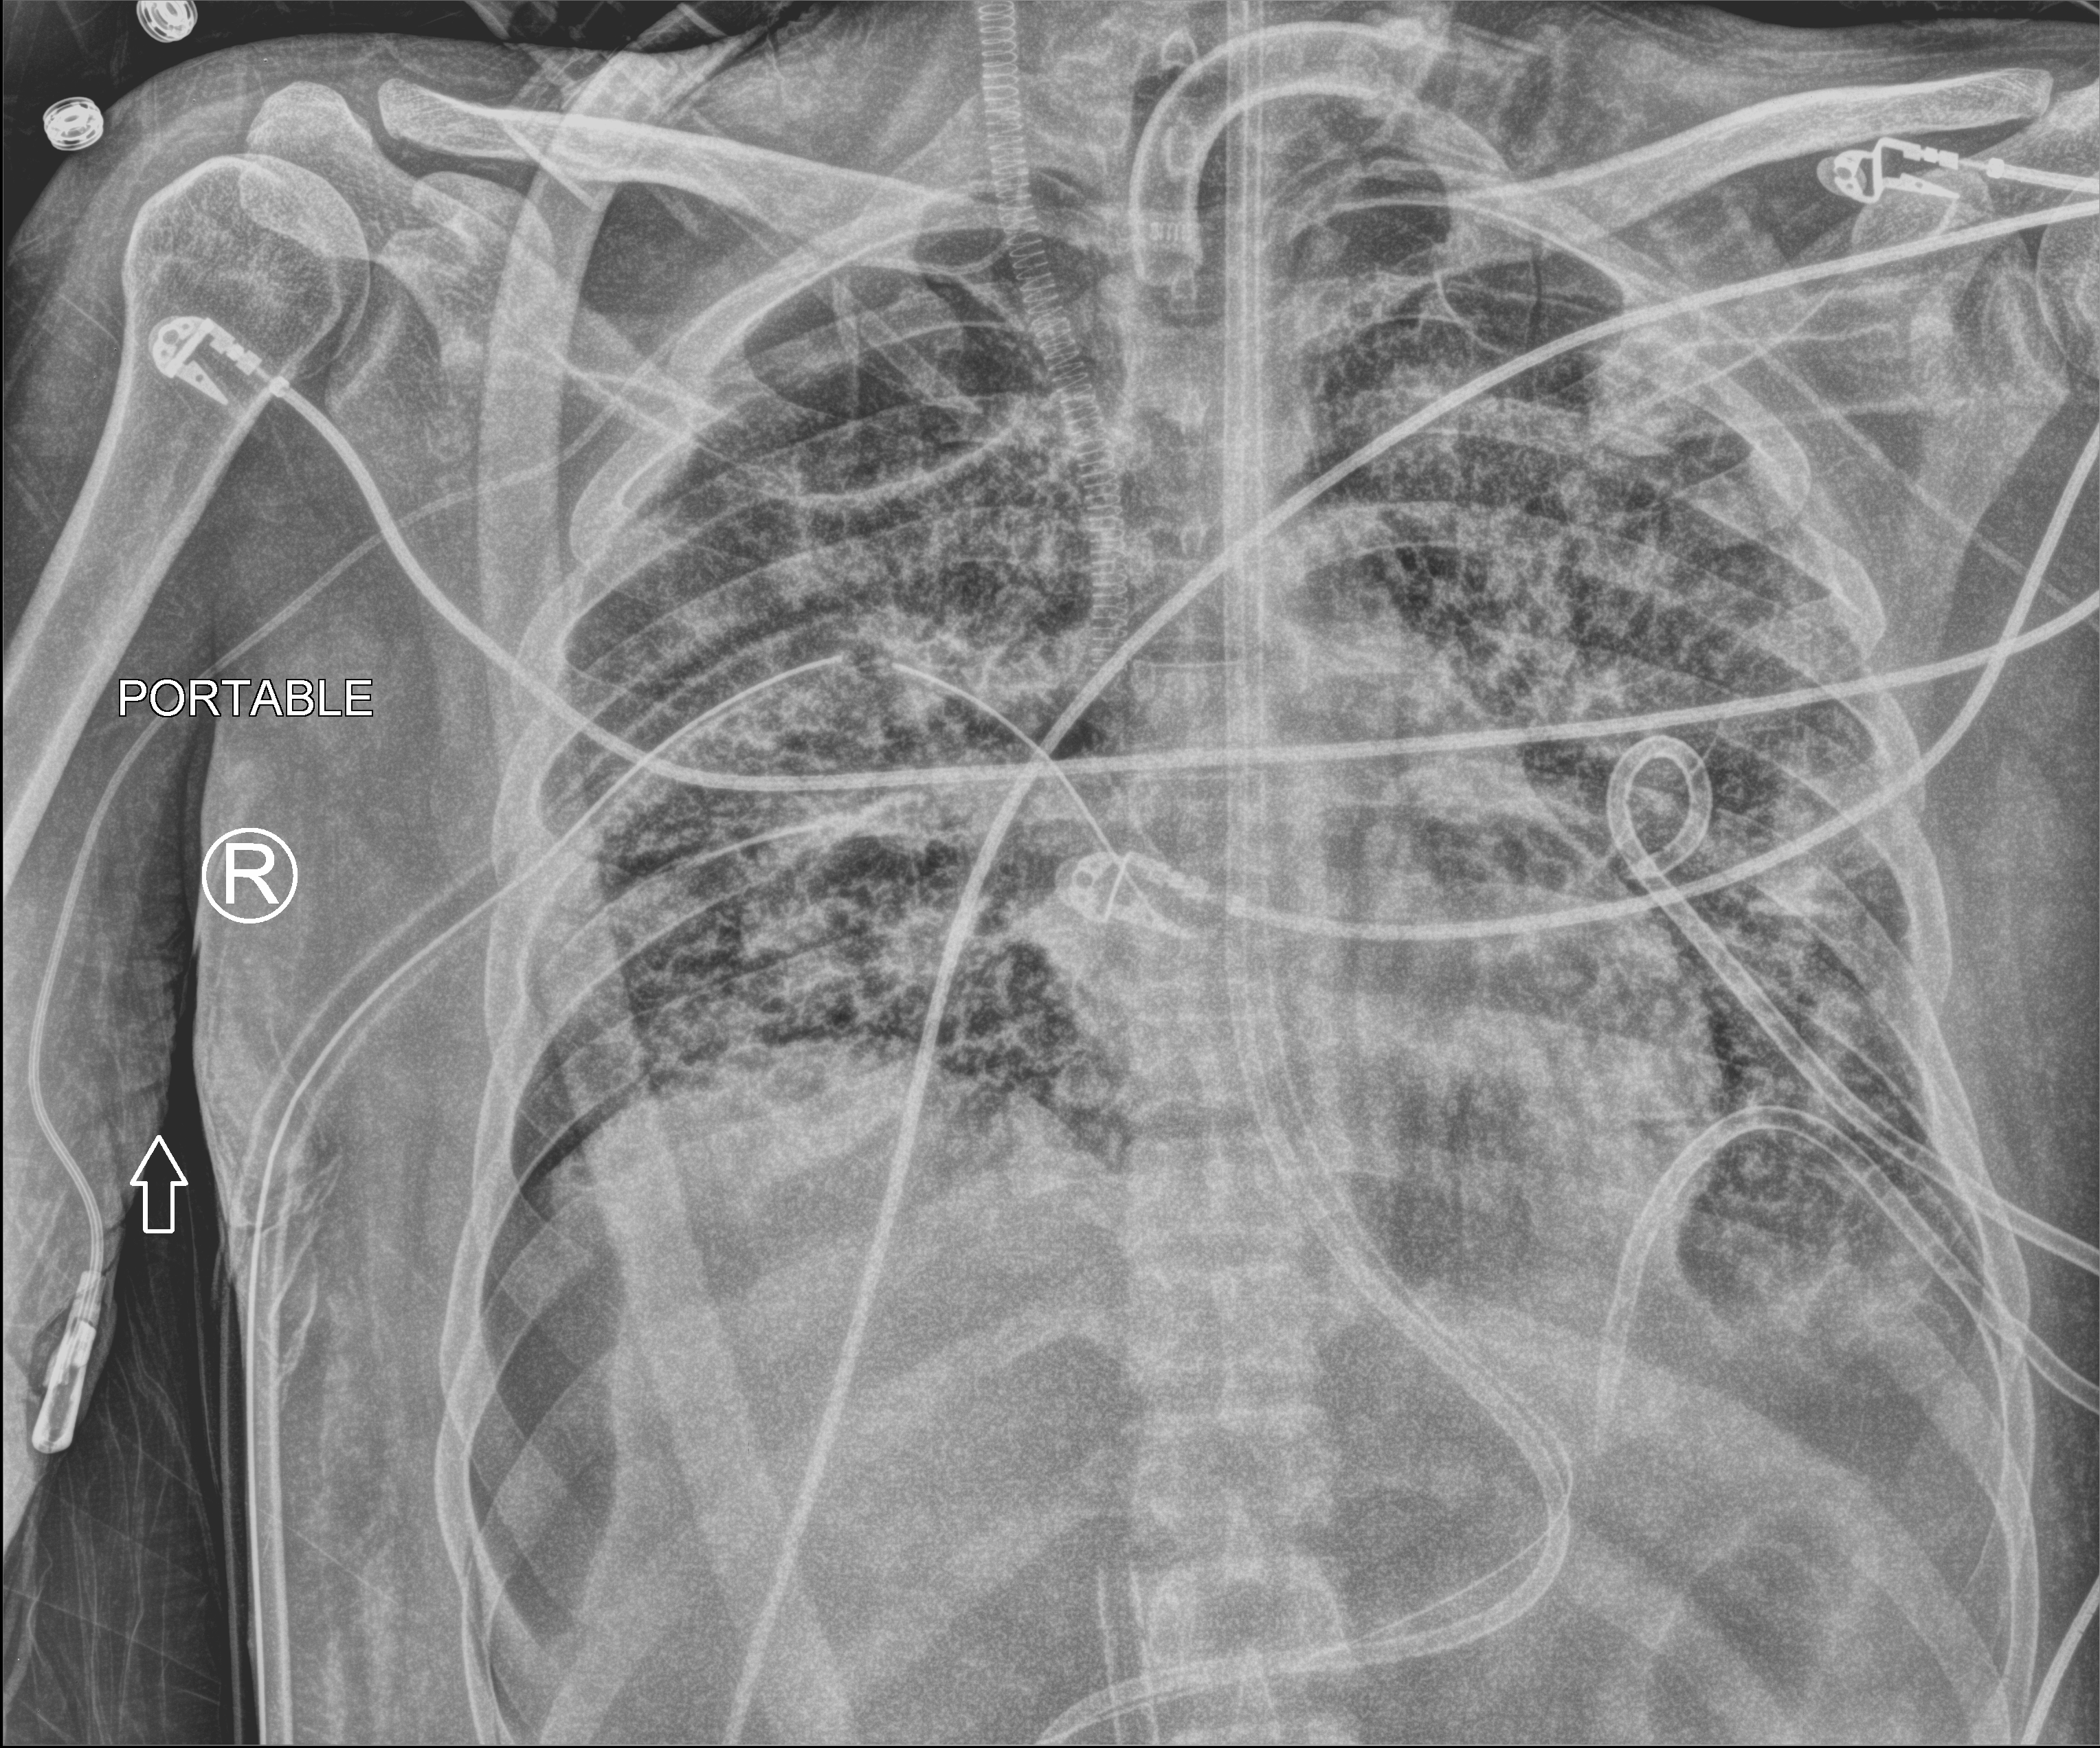
Chest X-ray (portable); anteroposterior (AP) projection. Adult patient hospitalised with COVID-19, age 18–59 years.
Hospital-stay facts (about this admission, not read from this image; timing relative to this image not recorded): admitted to intensive care during this hospital stay: yes; length of hospital stay: 60 days.